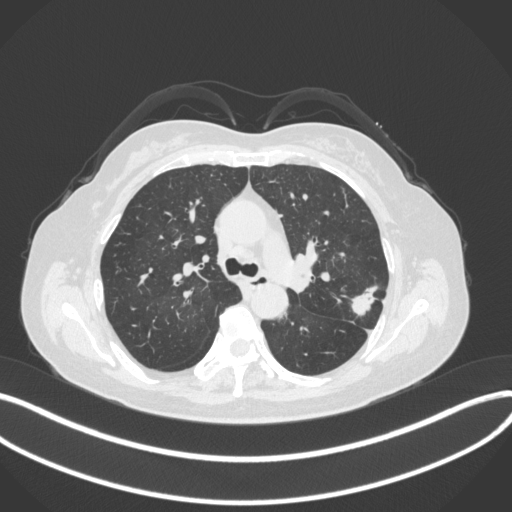
Chest CT, one axial slice. Position 222 of 330 along the scan axis. 120 kVp. Lung window (W 1500 / L -600 HU). 1 mm slice thickness. 512 × 512 image matrix, field of view 400 × 400 mm. Female patient, age 60 years. From the clinical record (not read from this slice): clinical TNM (as recorded): T1c N0 M0.
Outlined on this slice (rectangle marked by the reading radiologist):
- lung tumour (recorded histology: adenocarcinoma): bounding box (x1, y1, x2, y2) in pixels: (344, 277, 383, 319)